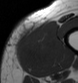
MRI of an extremity soft-tissue mass, one axial slice. Slice 10 of 43 in the series (ordered by position). MR volume resampled by the dataset authors to the PET/CT grid (not the native acquisition matrix). 3.27 mm slice thickness. 78 × 83 image matrix. Male patient. Case-level facts recorded for this patient, not image findings: histological type: pleiomorphic leiomyosarcoma; grade: high; site of the primary tumour: left thigh.
Outlined on this slice (expert contour drawn on MRI and transferred to this co-registered scan by the dataset authors):
- gross tumour volume including surrounding oedema: bounding box [x1, y1, x2, y2] px = [18, 21, 58, 71]
- gross tumour volume (mass): [18, 24, 55, 59]